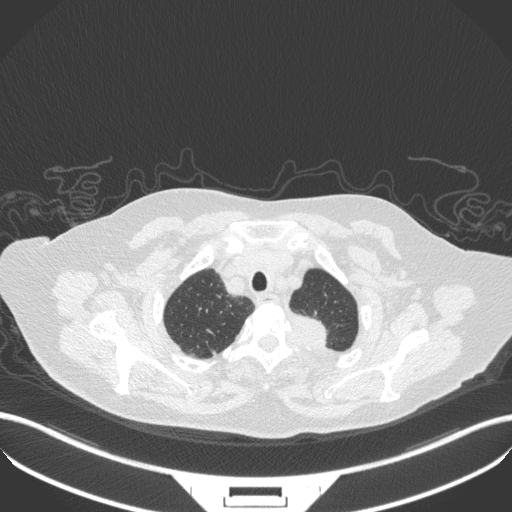
Chest CT, one axial slice; slice 303 of 353 in the series (ordered by position); reconstruction kernel B31f; 100 kVp; lung window (W 1500 / L -600 HU); 512 × 512 image matrix, field of view 400 × 400 mm. Female patient, age 81 years. From the clinical record (not read from this slice): clinical TNM (as recorded): T2a N0 M0.
Outlined on this slice (rectangle marked by the reading radiologist):
- lung tumour (recorded histology: adenocarcinoma): box from (x=289, y=309) to (x=338, y=349) px